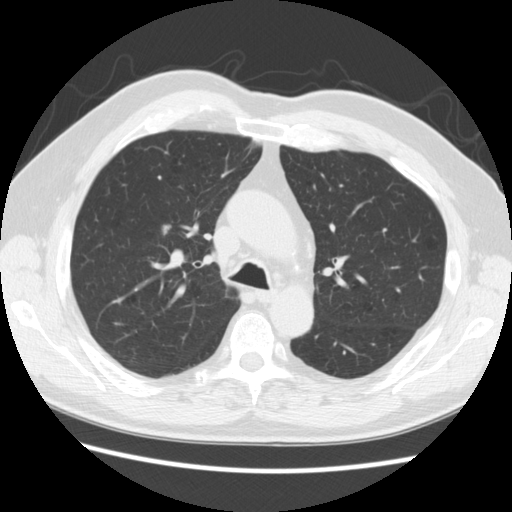
Axial slice from a low-dose chest CT screening exam; baseline annual screen; lung window (W 1500 / L -600 HU); 2.5 mm slice thickness; standard (soft-tissue) reconstruction kernel (STANDARD); 512 × 512 image matrix. Male, age 69 years at enrolment. Former smoker at enrolment.
- Expert reader's lesion annotation, bounding box [x1, y1, x2, y2] px = [148, 218, 194, 252].
- Screening reader's record for this exam (one nodule recorded; not confirmed to be the boxed lesion): non-calcified nodule or mass ≥4 mm, right upper lobe, 9 × 7 mm, poorly defined margins, soft tissue attenuation.
- Later outcome: lung cancer diagnosed 50 days after this screen — adenocarcinoma, NOS, right upper lobe, moderately differentiated (G2), stage IA (AJCC 6th edition), 9 mm at pathology.